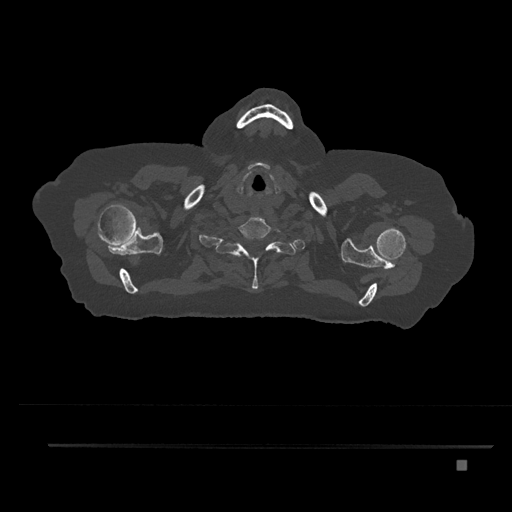
CT including the spine, one axial slice; slice 708 of 797 in the series (ordered by position); bone window (W 1800 / L 400 HU); 0.5 mm slice thickness; 512 × 512 image matrix. Female patient, age 76 years. Case-level facts recorded for this patient, not image findings: primary cancer: lung; vertebrae with lytic lesions (as recorded): T11, L3.
Structures marked on this image (semi-automatic segmentation, software-assisted and operator-edited):
- T1 vertebra: box from (x=224, y=237) to (x=284, y=289) px